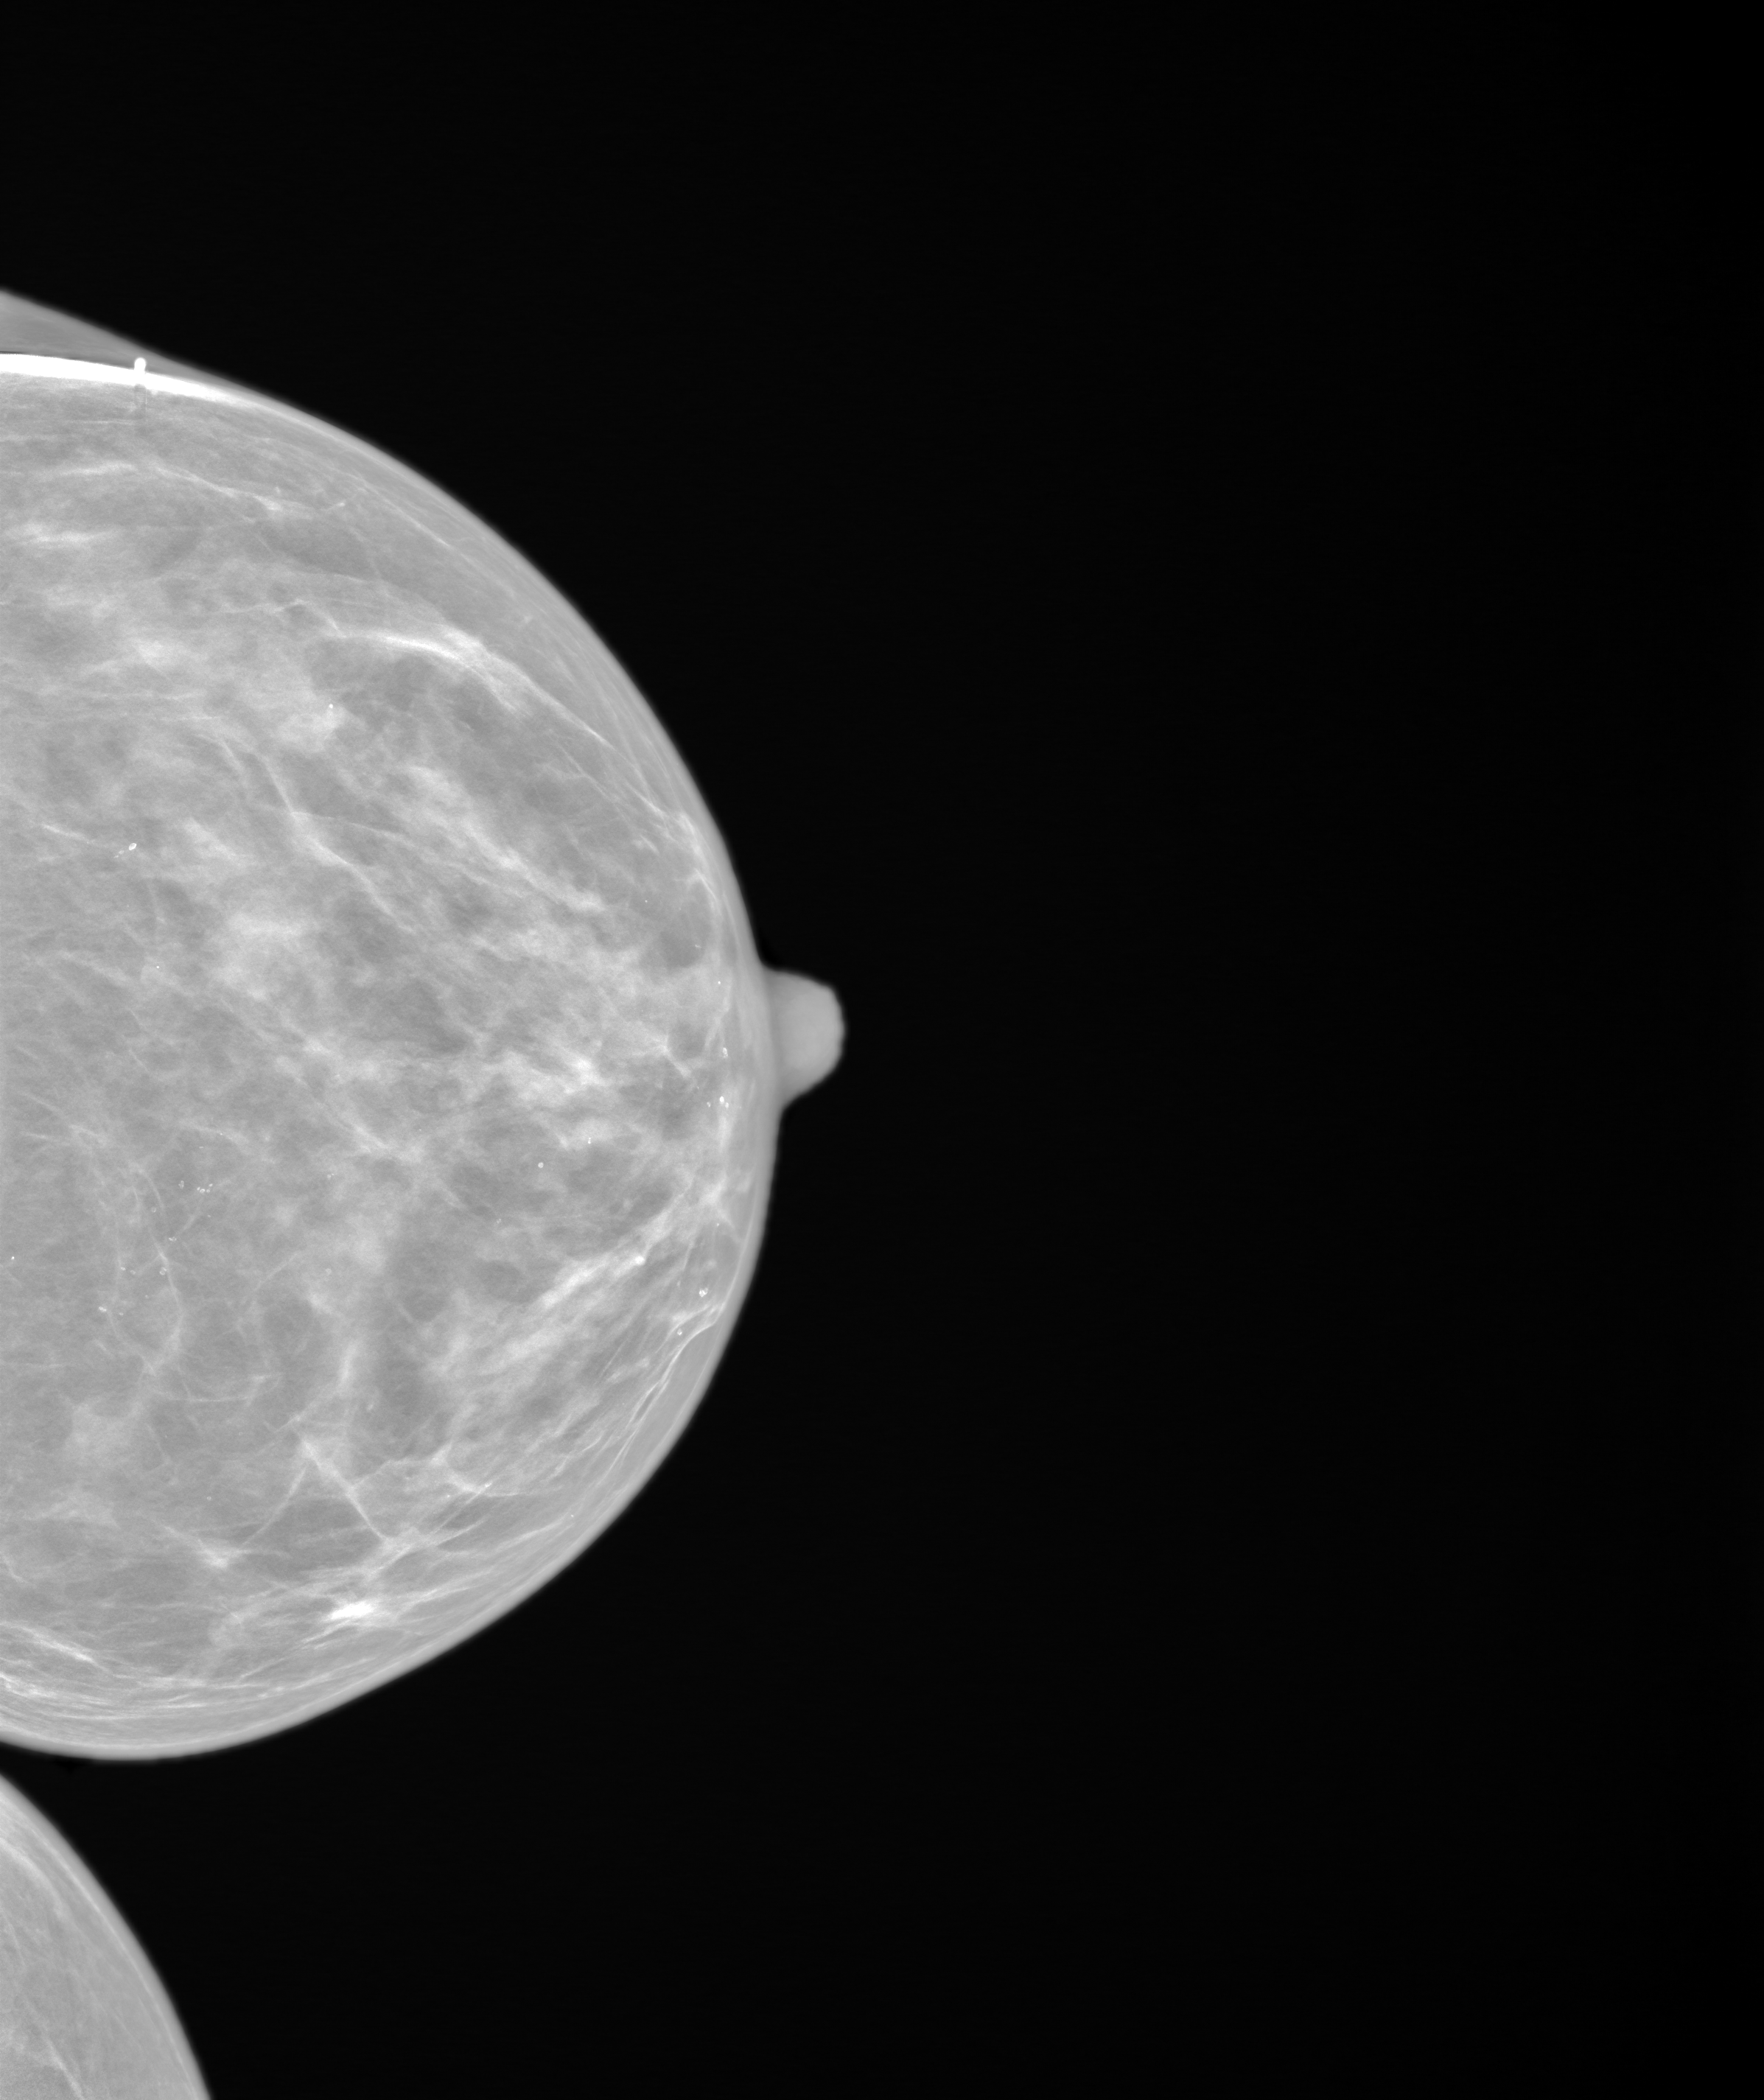
Diagnostic work-up study. Female patient, age 47 years.
Image type: synthesized 2-D view from tomosynthesis. Breast: left. Projection: cranio-caudal projection.